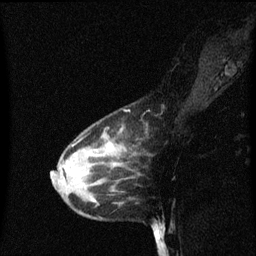
Breast MRI (dynamic contrast-enhanced), one sagittal slice. Dynamic contrast-enhanced series, image 2 of 3 at this slice position (ordered by acquisition). 1.5 T. TE 4.2 ms, TR 8.4 ms. 2 mm slice thickness. 256 × 256 image matrix, field of view 200 × 200 mm. Patient: female, 38 years. Case-level facts recorded for this patient, not image findings: setting: breast cancer imaged before/during neoadjuvant chemotherapy; receptor status: HR-positive, HER2-negative.
Outlined on this slice (semi-automatically segmented with operator editing):
- analysis volume of interest (the breast-tissue region the enhancement analysis was run in; not a lesion): box from (x=50, y=118) to (x=137, y=205) px
- tumour enhancement mask (voxels above the 70 % enhancement threshold inside the analysis volume of interest): (x=66, y=144)–(x=113, y=169)